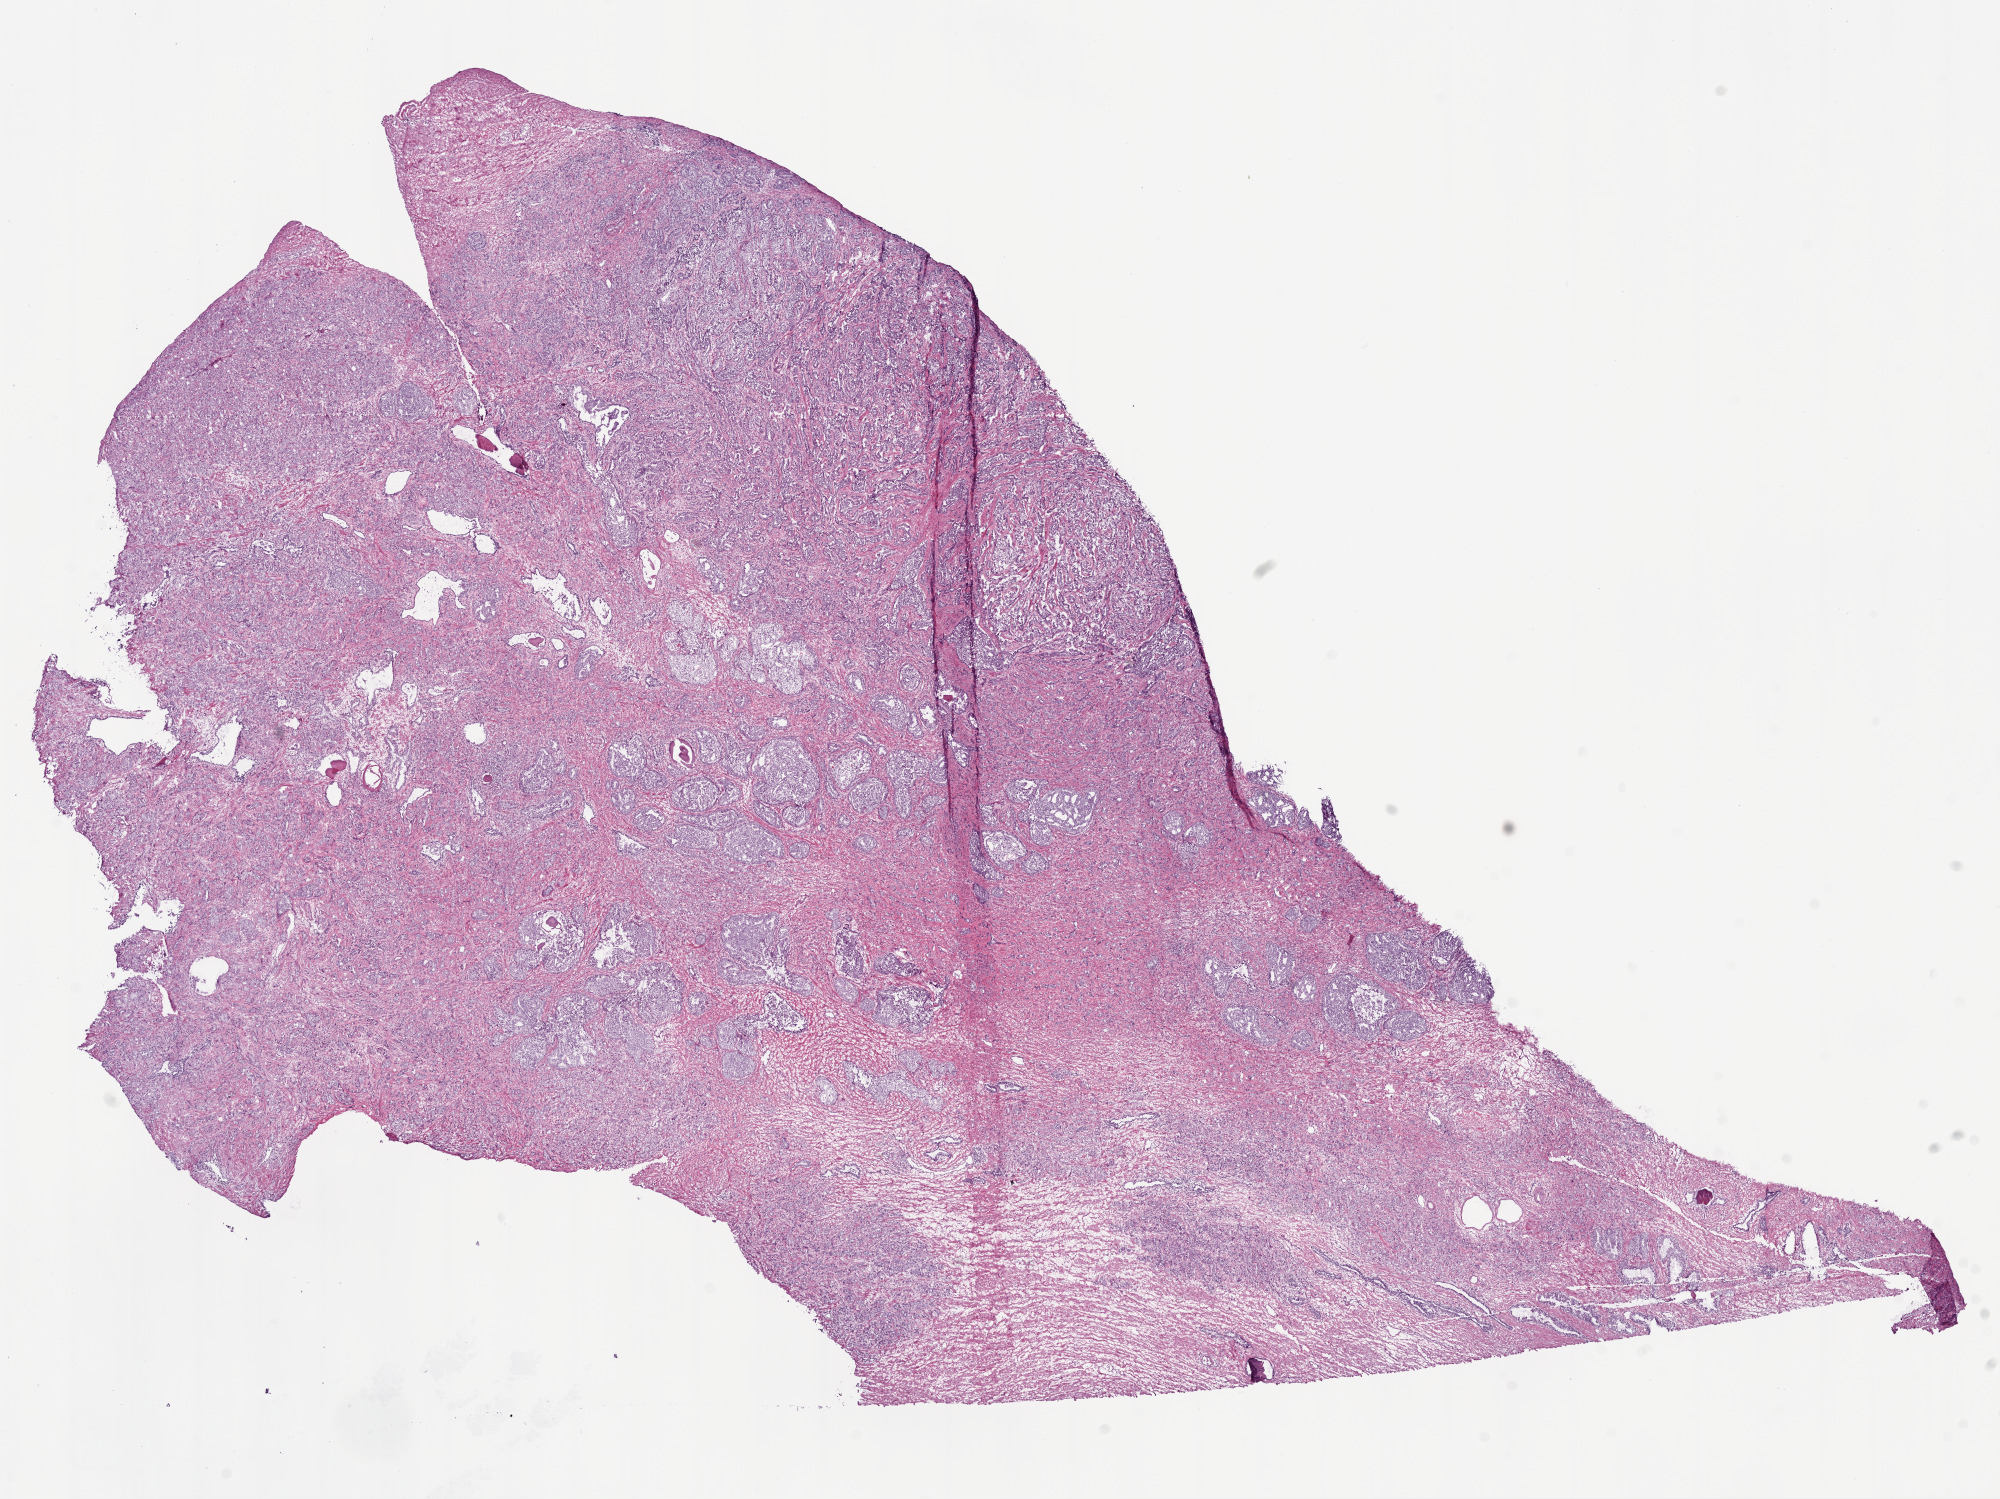
Whole-slide histology image, H&E — whole scanned area (about 16.0 x 12.0 mm, from a 20x scan) shown as a low-resolution overview, frozen section, prostate, primary tumour sample. Male patient; age at initial diagnosis 57 years. Gleason score: 9 (4+5). Pathologist review of this section (percent, as recorded): tumour cells 70%, tumour nuclei 80%, normal cells 10%, stromal cells 20%, necrosis 0%. Inflammatory infiltration, as recorded: lymphocyte infiltration 2%, monocyte infiltration 0%, neutrophil infiltration 0%.
- laterality: bilateral
- diagnosis: Acinar cell carcinoma (prostate gland)
- lymph nodes positive (case pathology): 0 of 17 examined